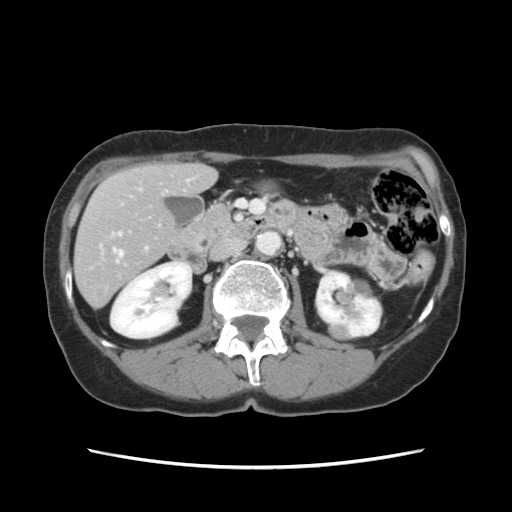
Contrast-enhanced abdominal CT, one axial slice. Slice 49 of 120 in the series (ordered by position). Intravenous contrast given. Soft-tissue window (W 400 / L 40 HU). 2.5 mm slice thickness. 512 × 512 image matrix, field of view 330 × 330 mm. Female patient, age 70 years. From the clinical record (not read from this slice): diagnosis: colorectal cancer liver metastases, imaged before liver resection; multiple liver metastases: no; largest metastasis: 2.5 cm.
Structures marked on this image (outlined manually by an expert reader):
- hepatic veins: bounding box <113,249,123,262> (left, top, right, bottom; pixels)
- liver: <76,164,215,307>
- planned liver remnant (the part of the liver to remain after resection): <76,164,215,307>
- portal vein (with intrahepatic branches): <101,180,190,250>